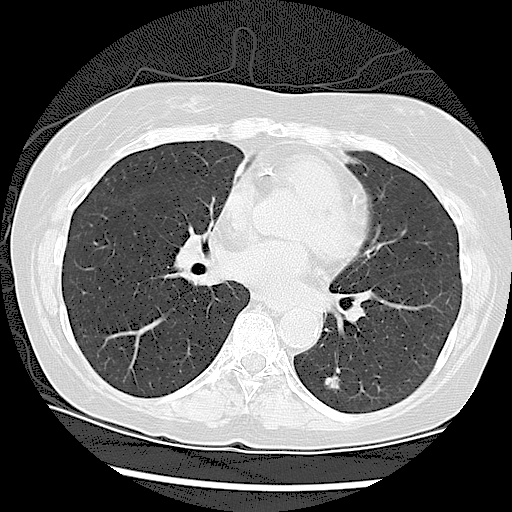
Low-dose screening chest CT, one axial slice; slice 49 of 108 in the series (ordered by position); reconstruction kernel LUNG; lung window (W 1500 / L -600 HU); 2.5 mm slice thickness; 512 × 512 image matrix.
Annotated regions visible in this slice (manually delineated by an expert):
- lesion 1 (tumor, lower lobe of left lung): bounding box (x1, y1, x2, y2) in pixels: (325, 376, 341, 393)